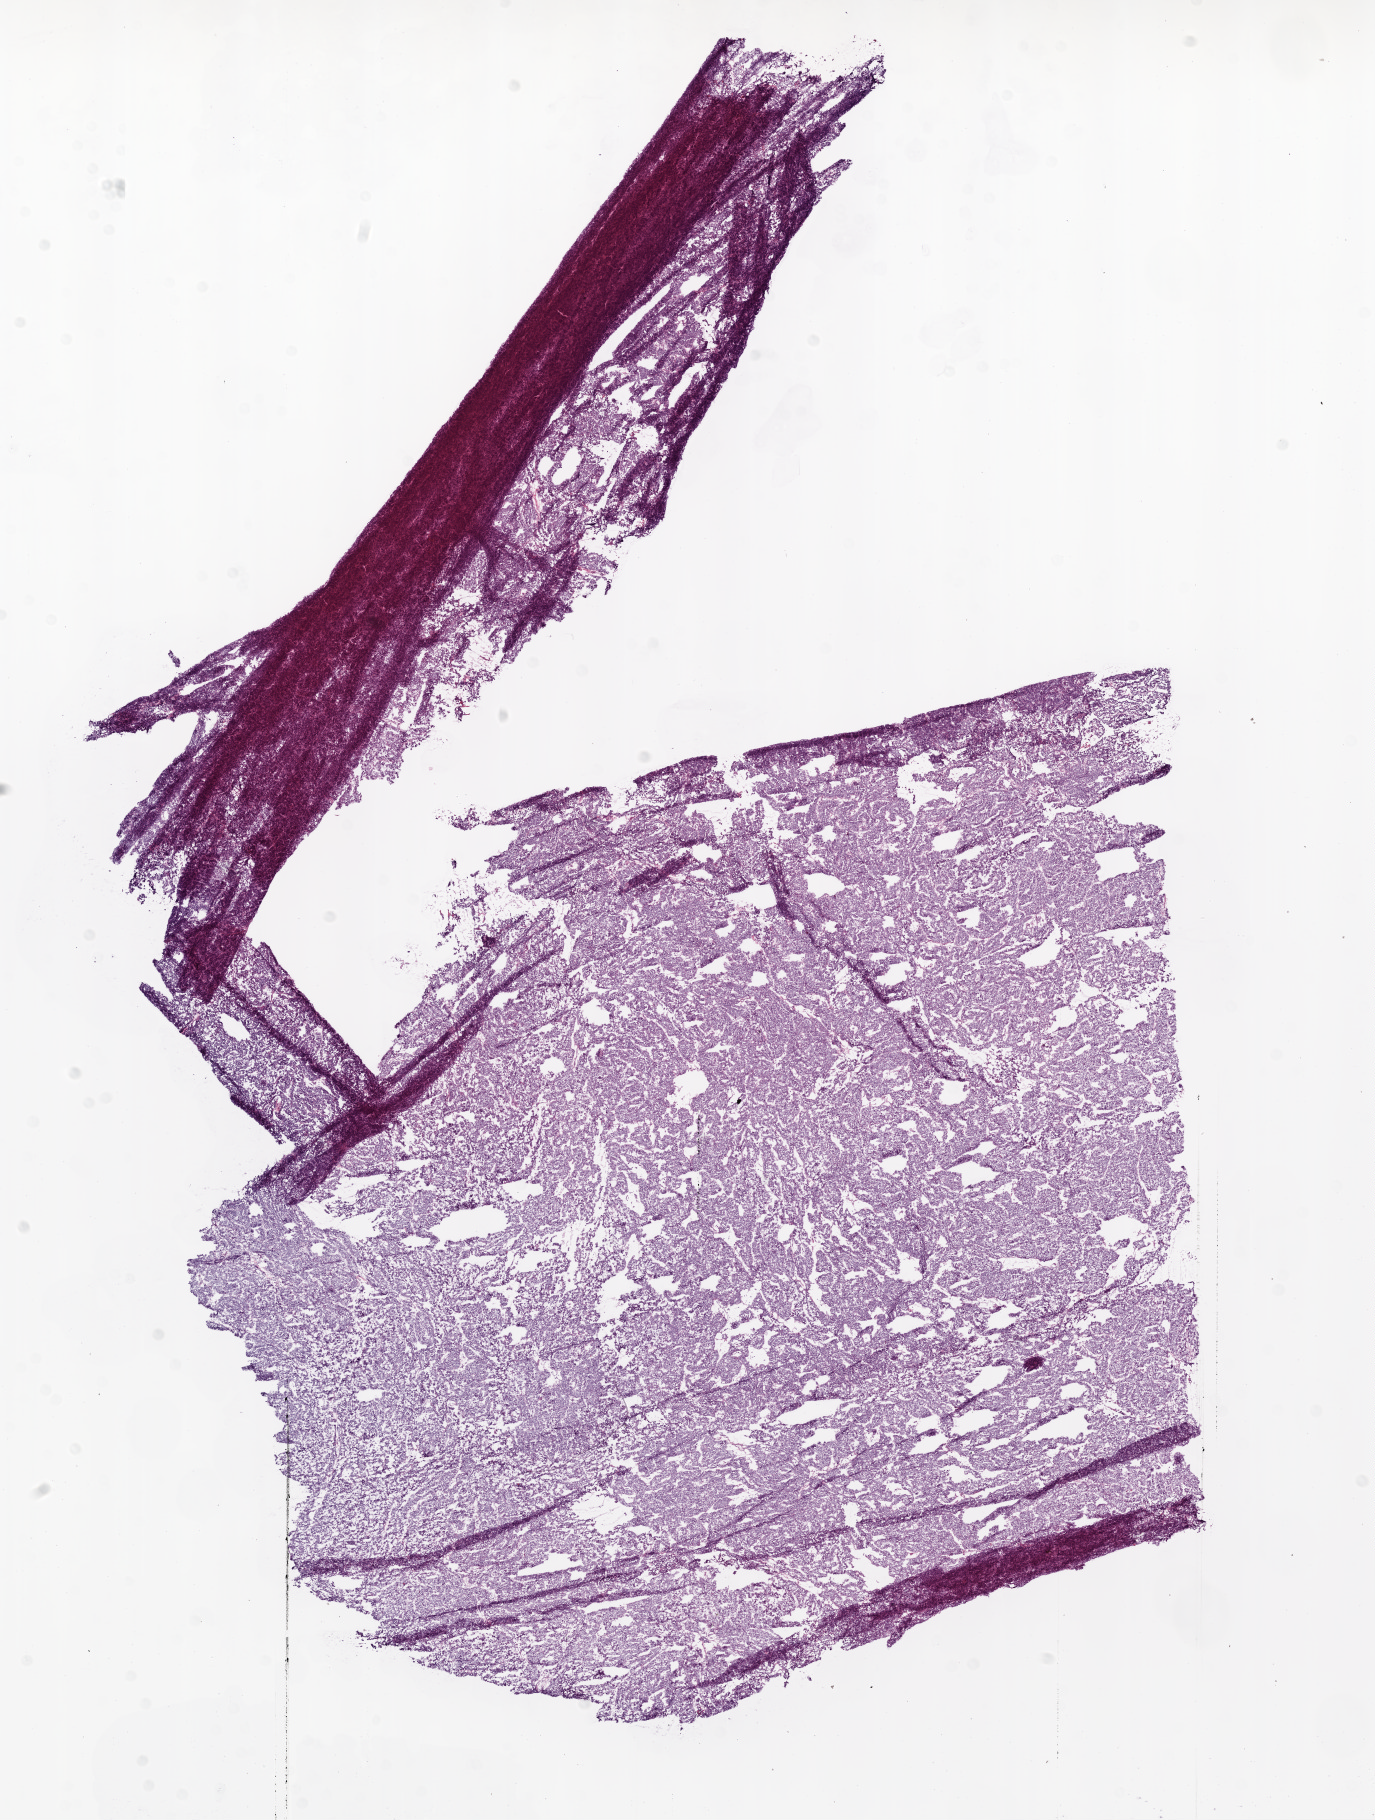
H&E whole-slide image — a low-resolution overview of the entire scanned area, about 11.0 x 14.6 mm (from a 20x scan); frozen section from the bottom of the tissue portion; recurrent tumour sample from the ovary. Female patient; age at initial diagnosis 55 years. Slide review estimates, as recorded: tumour cells 99%, tumour nuclei 99%, normal cells 0%, stromal cells 1%, necrosis 0%.
* this section: recurrent tumour
* patient diagnosis: Serous surface papillary carcinoma